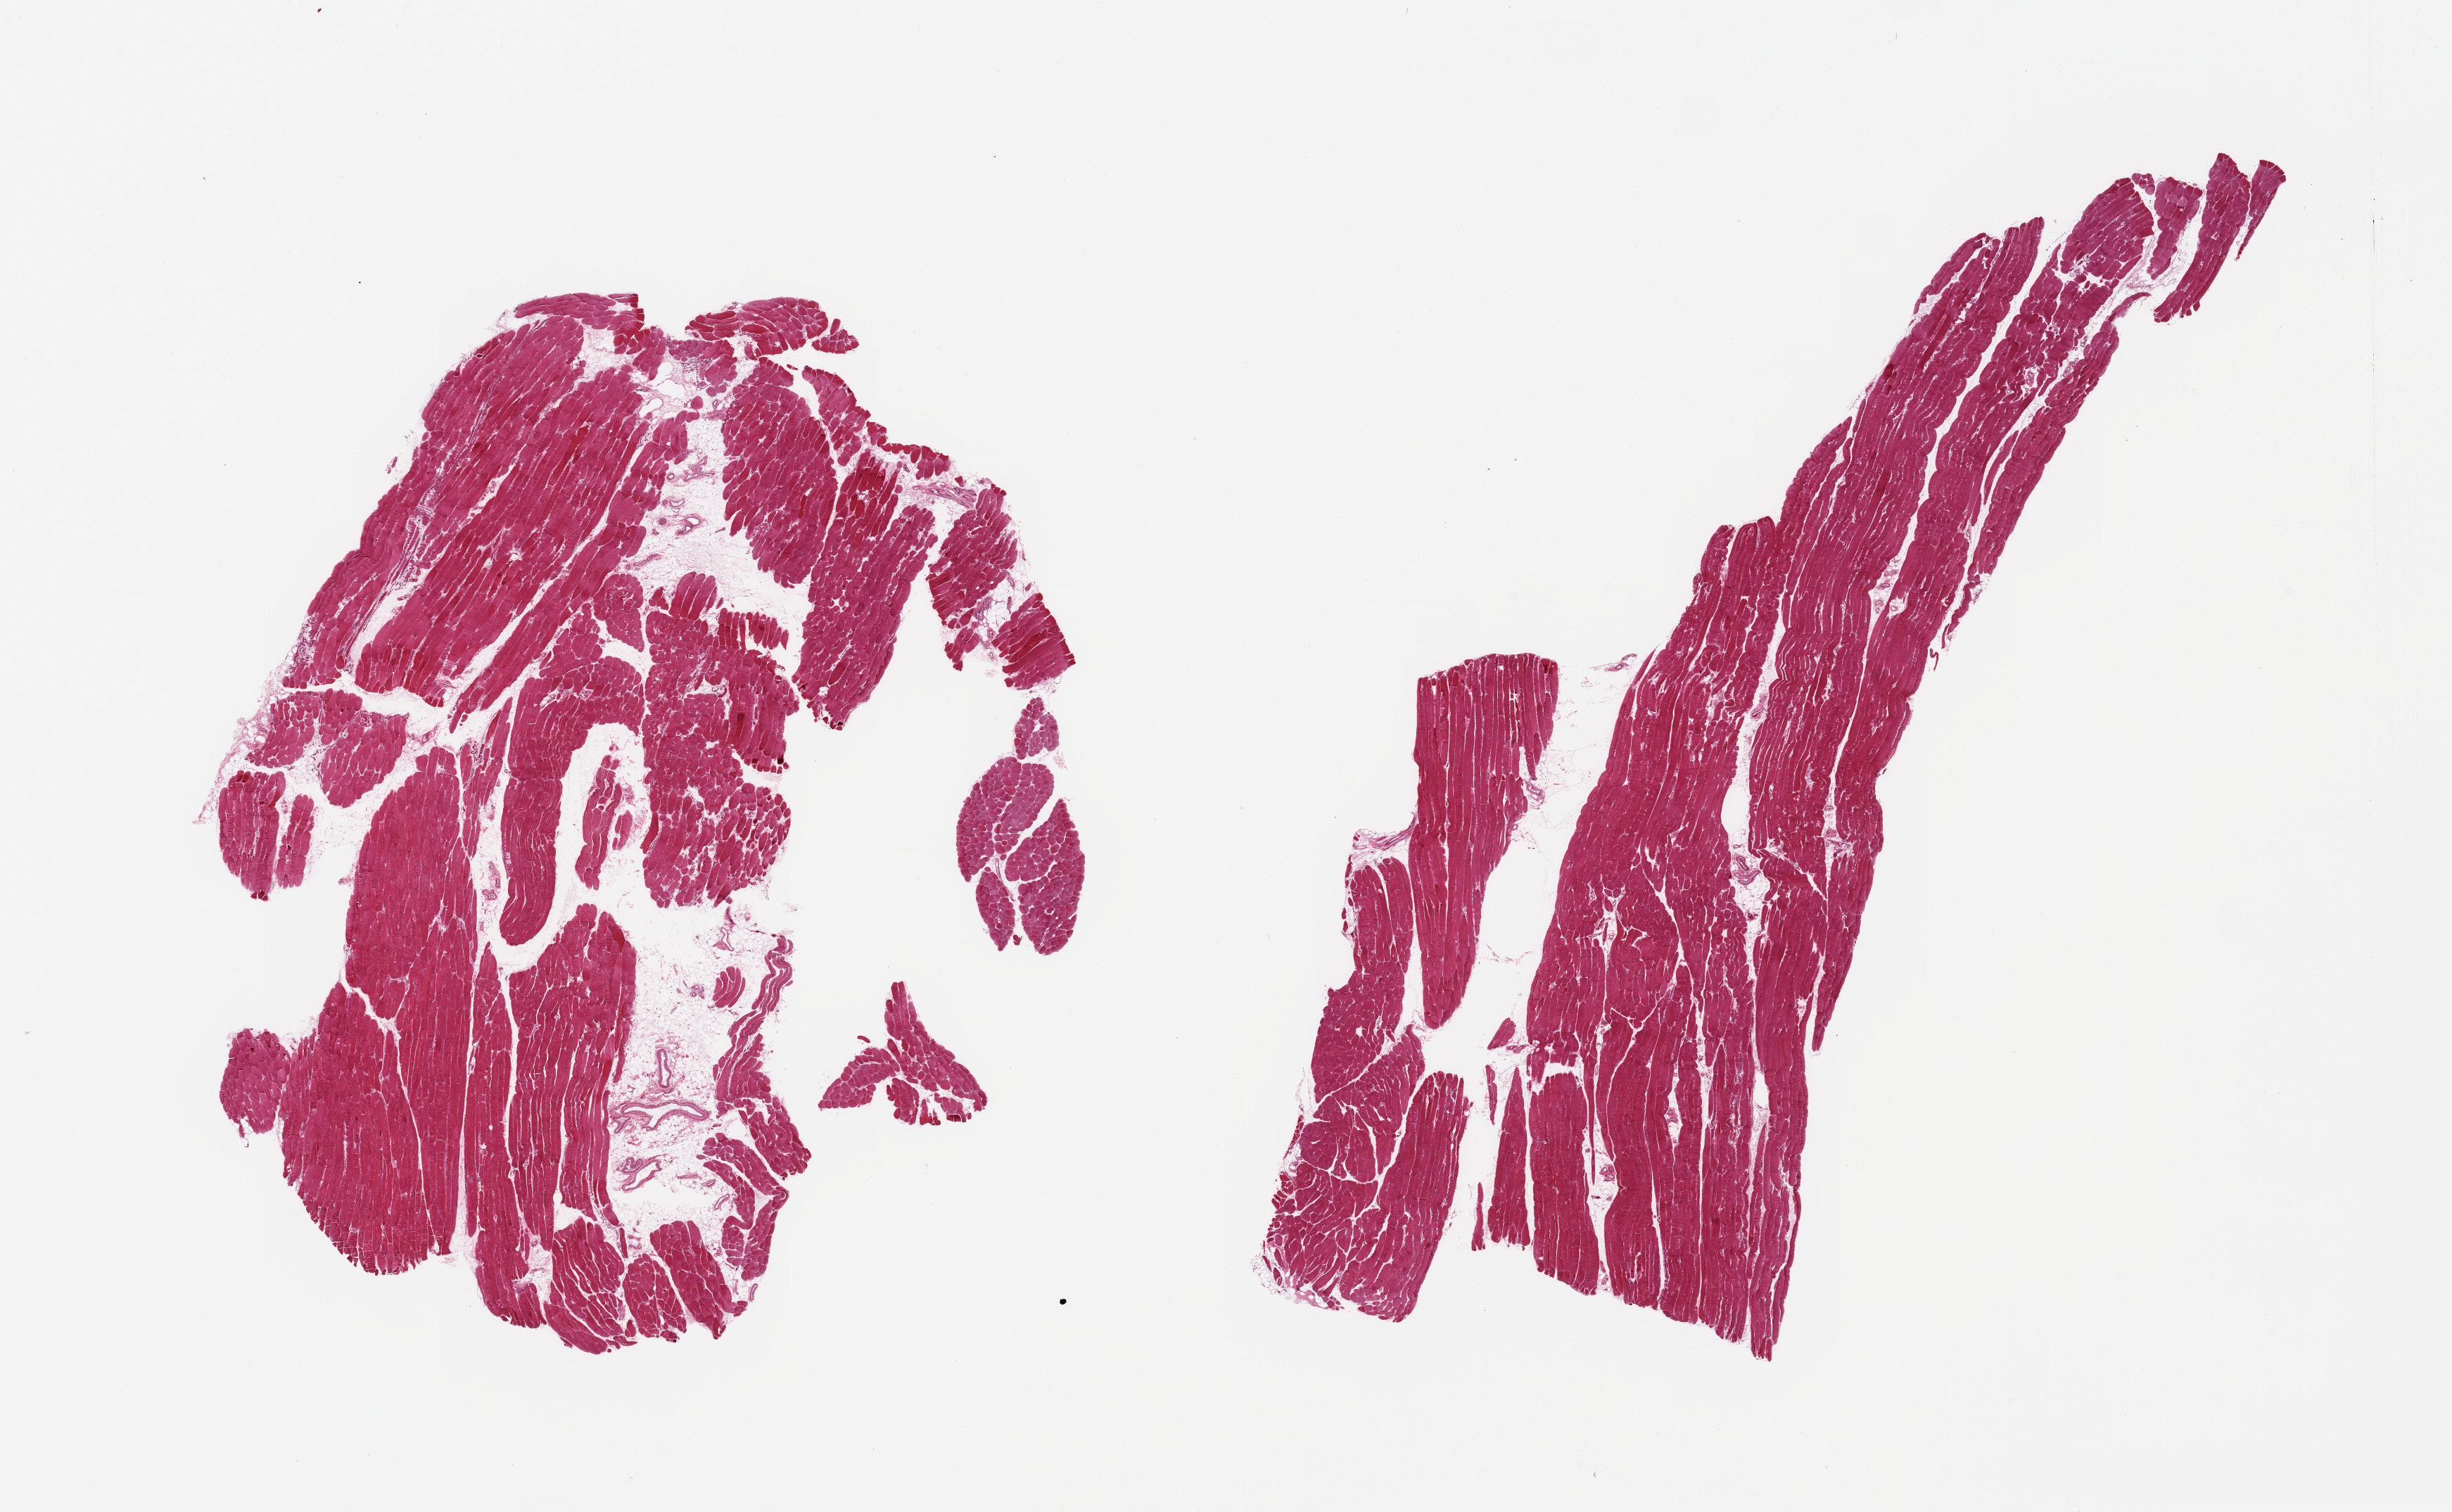
Digitized hematoxylin and eosin (H&E)-stained section, shown as a low-resolution overview of the whole scanned area (about 27.6 x 17.0 mm, slide scanned at 20x), PAXgene-fixed, paraffin-embedded tissue, target tissue: skeletal muscle, donor tissue sample.
Pathologist's review note for this sample: 2 pieces; up to 10% internal fat, some atrophy.